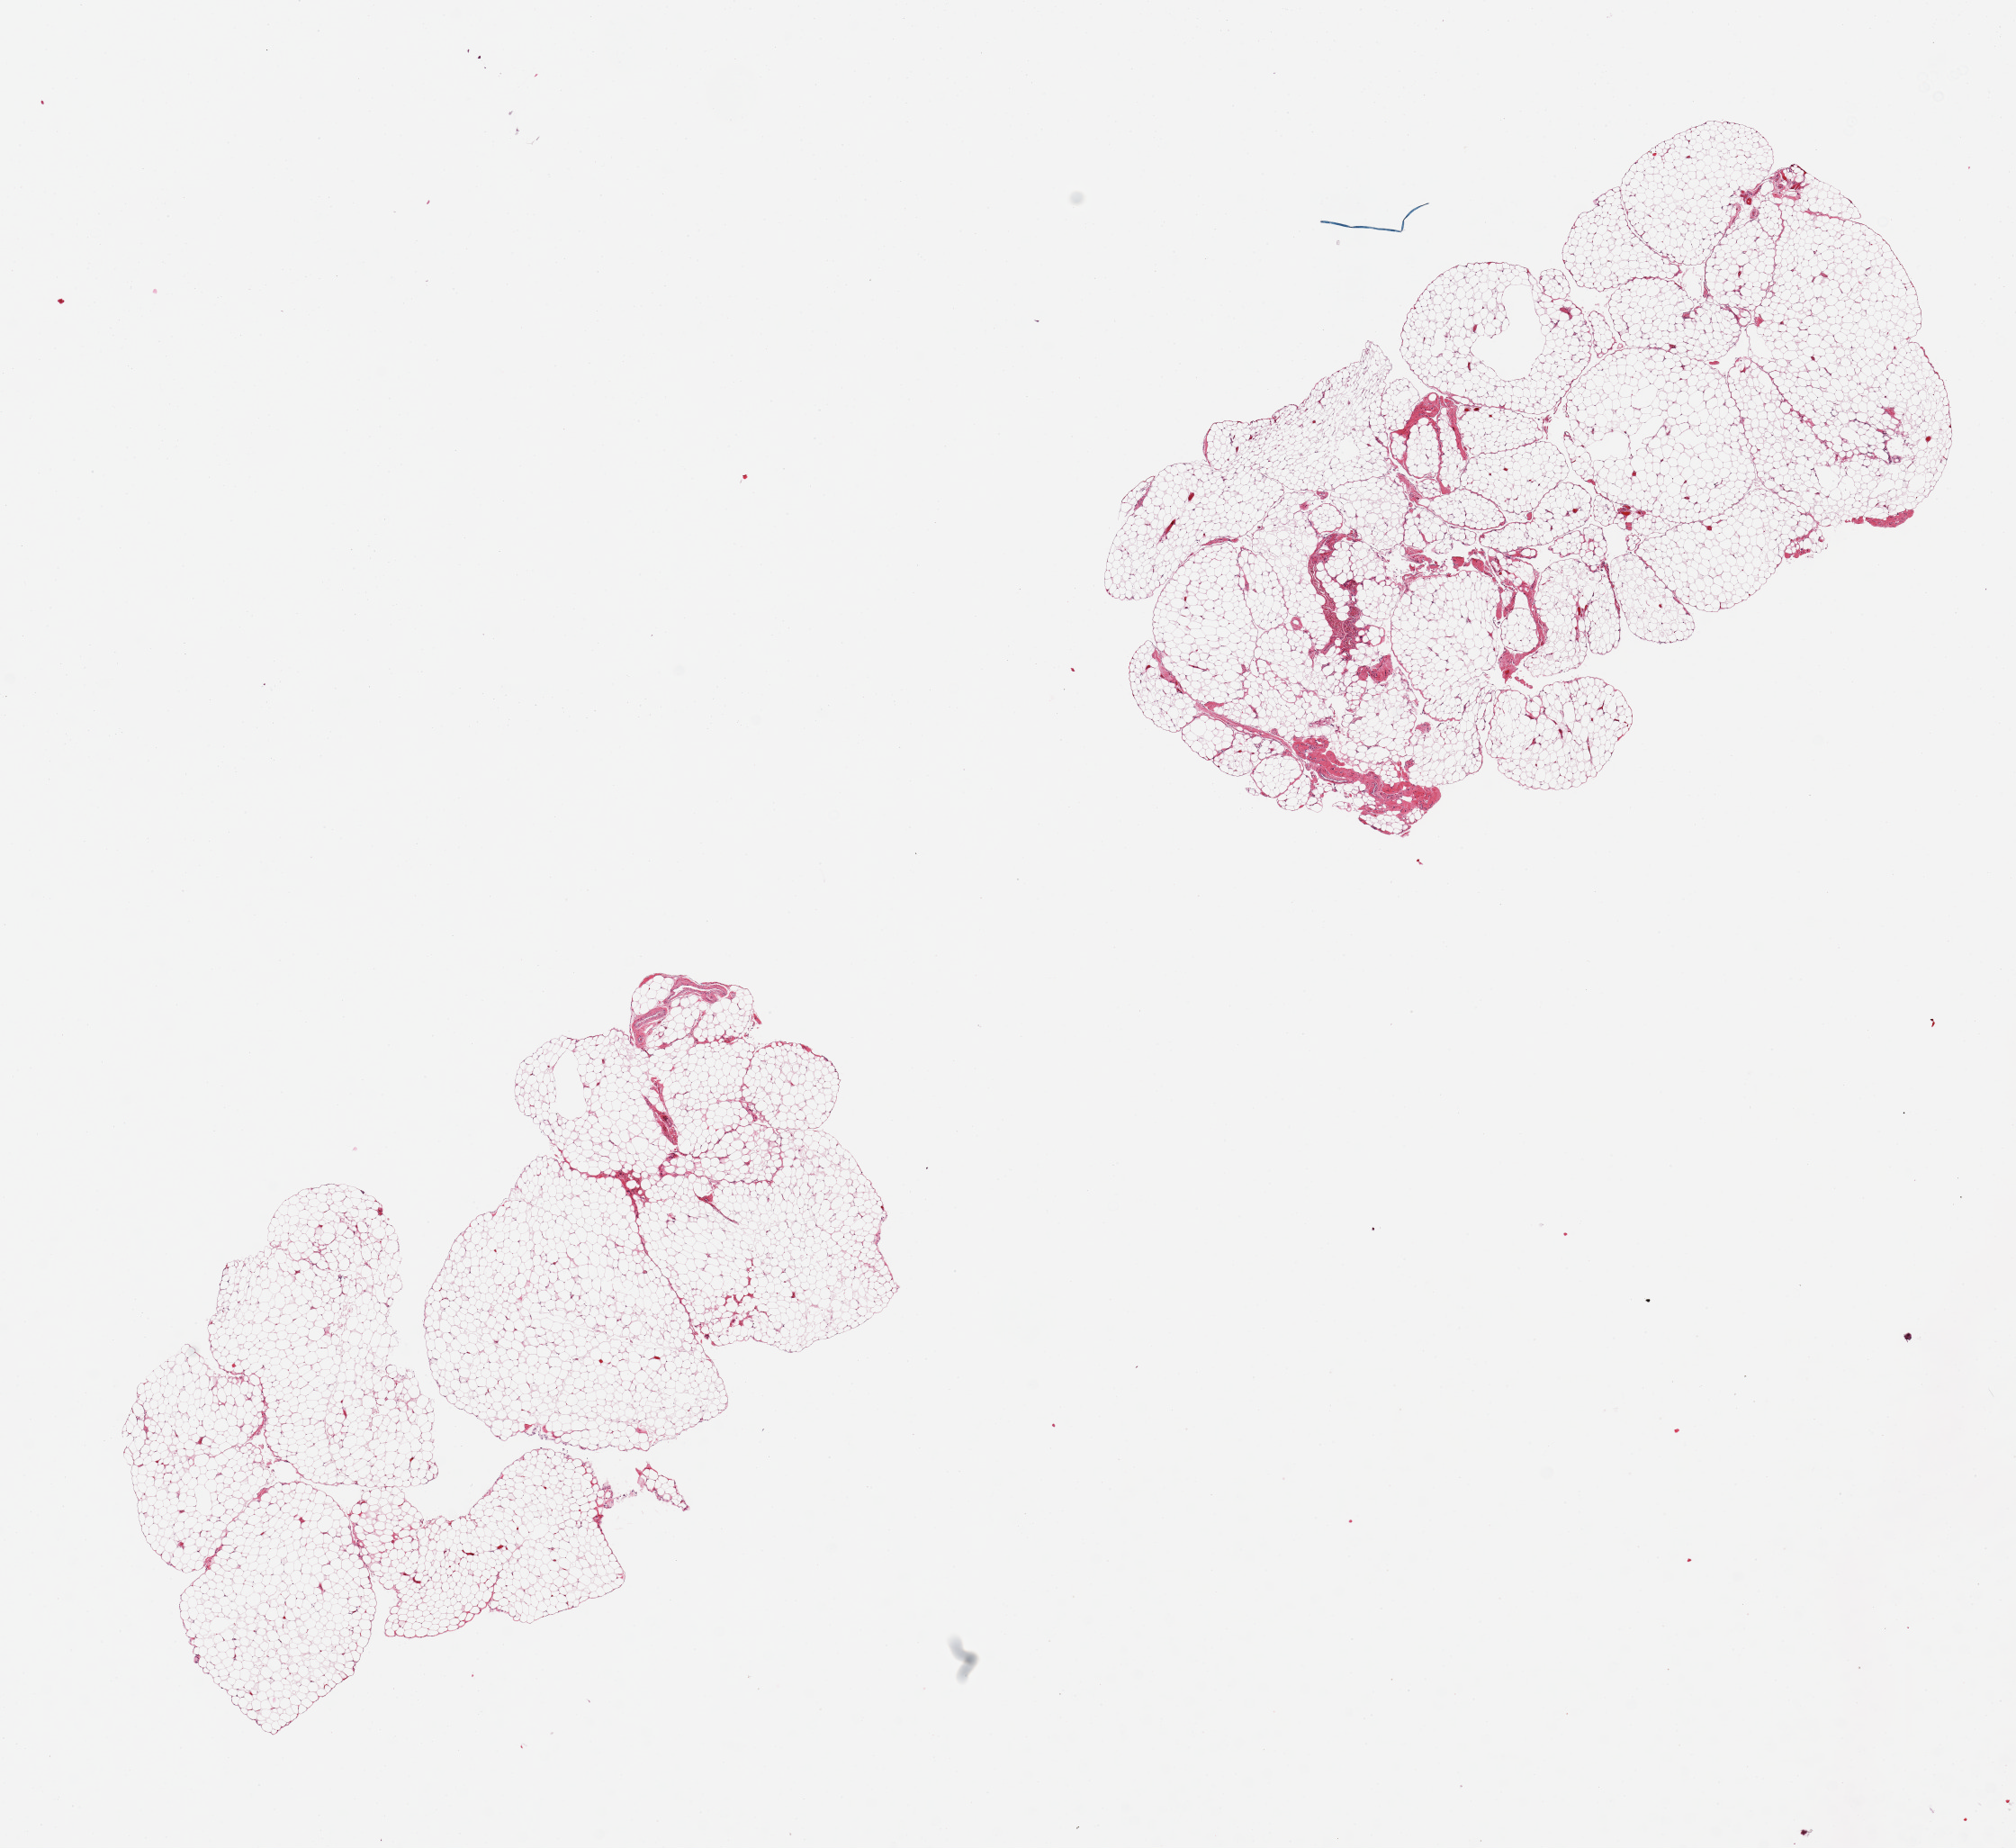
Whole-slide image, hematoxylin and eosin (H&E) stain, brightfield — shown as a low-resolution overview of the whole scanned area (about 17.7 x 16.2 mm, from a 20x scan), PAXgene-fixed paraffin-embedded (PFPE) section, sampled site (target tissue): omentum, donor tissue sample. Male donor.
Reviewer comment on this tissue sample: 2 pieces, ~5% fibro/fascia tissue.